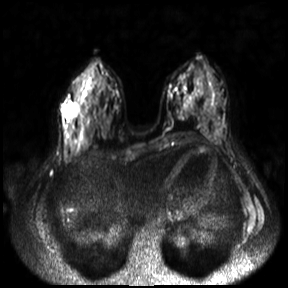
Breast MRI, one axial slice. Slice 13 of 30 in the series (ordered by position). Diffusion-weighted series; image 2 of 4 stored at this slice position (different b-values; order by instance number). 3 T. 4 mm slice thickness. 288 × 288 image matrix. Female patient.
Structures marked on this image (expert manual segmentation):
- tumour on diffusion-weighted imaging: bounding box [x1, y1, x2, y2] px = [62, 101, 80, 118]